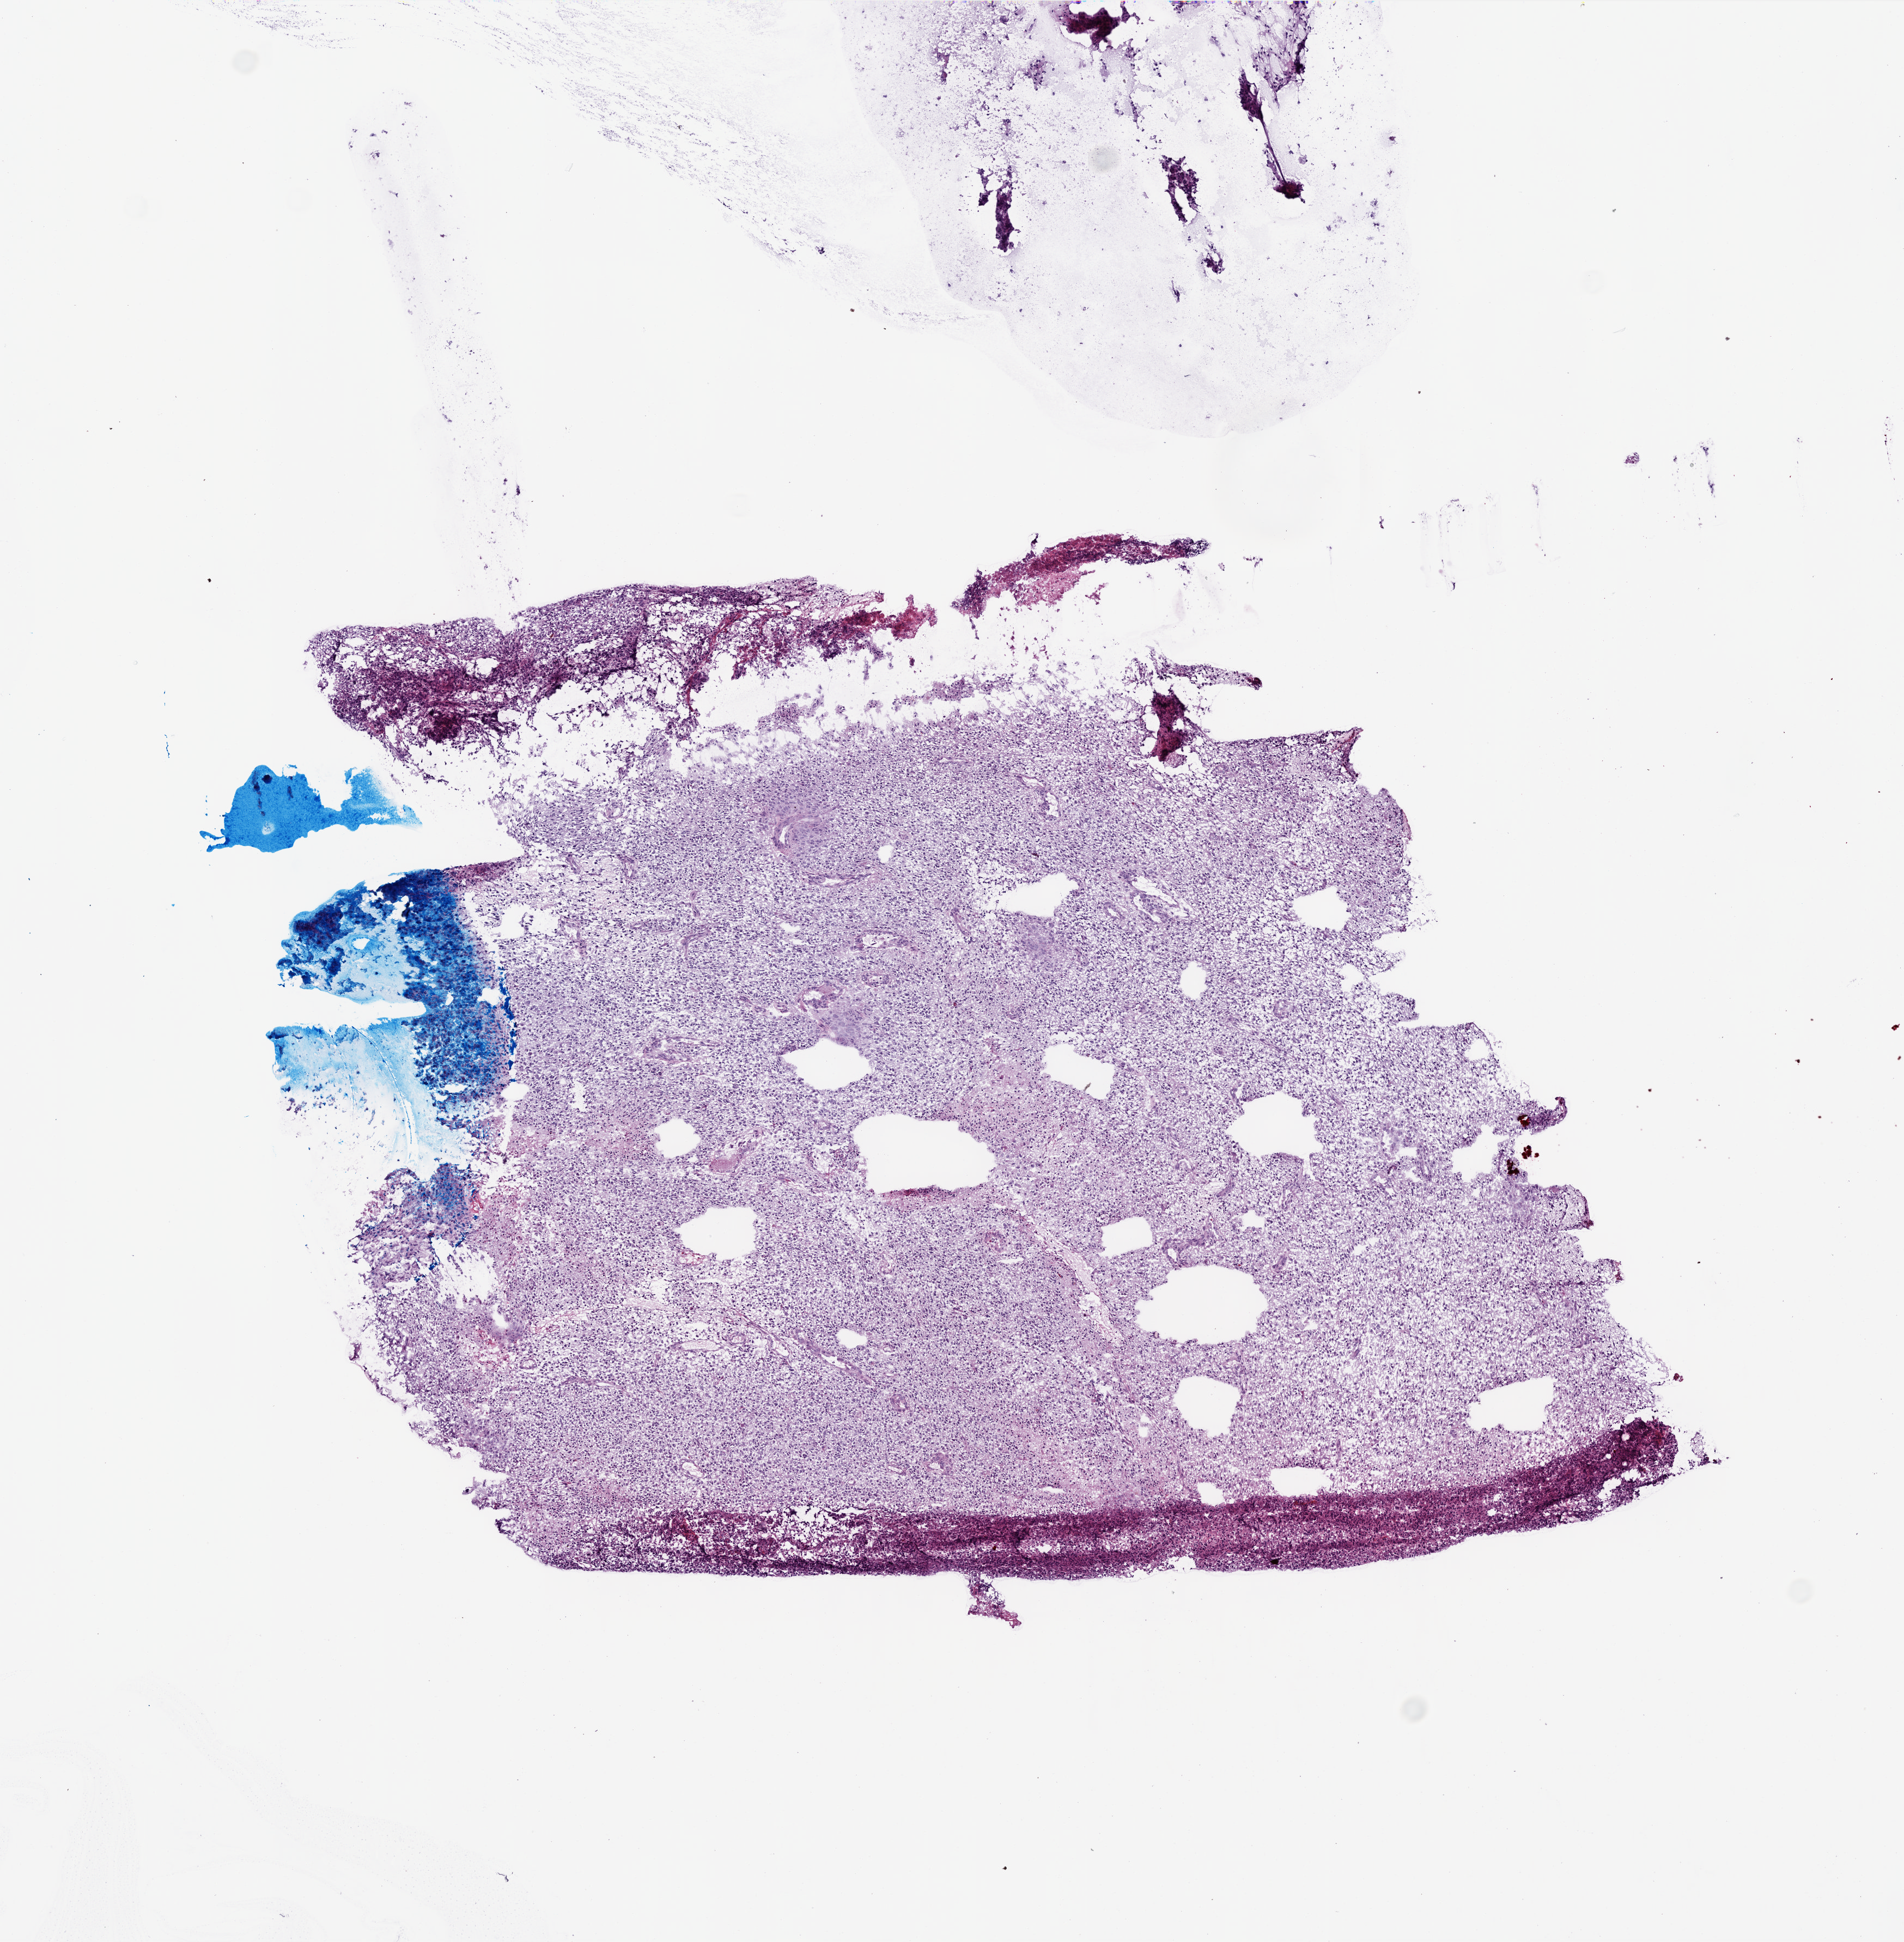
Digitized H&E-stained tissue section (whole slide) — whole scanned area (about 7.0 x 7.1 mm, from a 20x scan) shown as a low-resolution overview; frozen section from the top of the tissue portion; brain, primary tumour sample. Male patient; age at initial diagnosis 74 years. Slide review estimates, as recorded: tumour cells 95%, tumour nuclei 95%, normal cells 0%, stromal cells 0%, necrosis 5%.
- histologic diagnosis: Glioblastoma